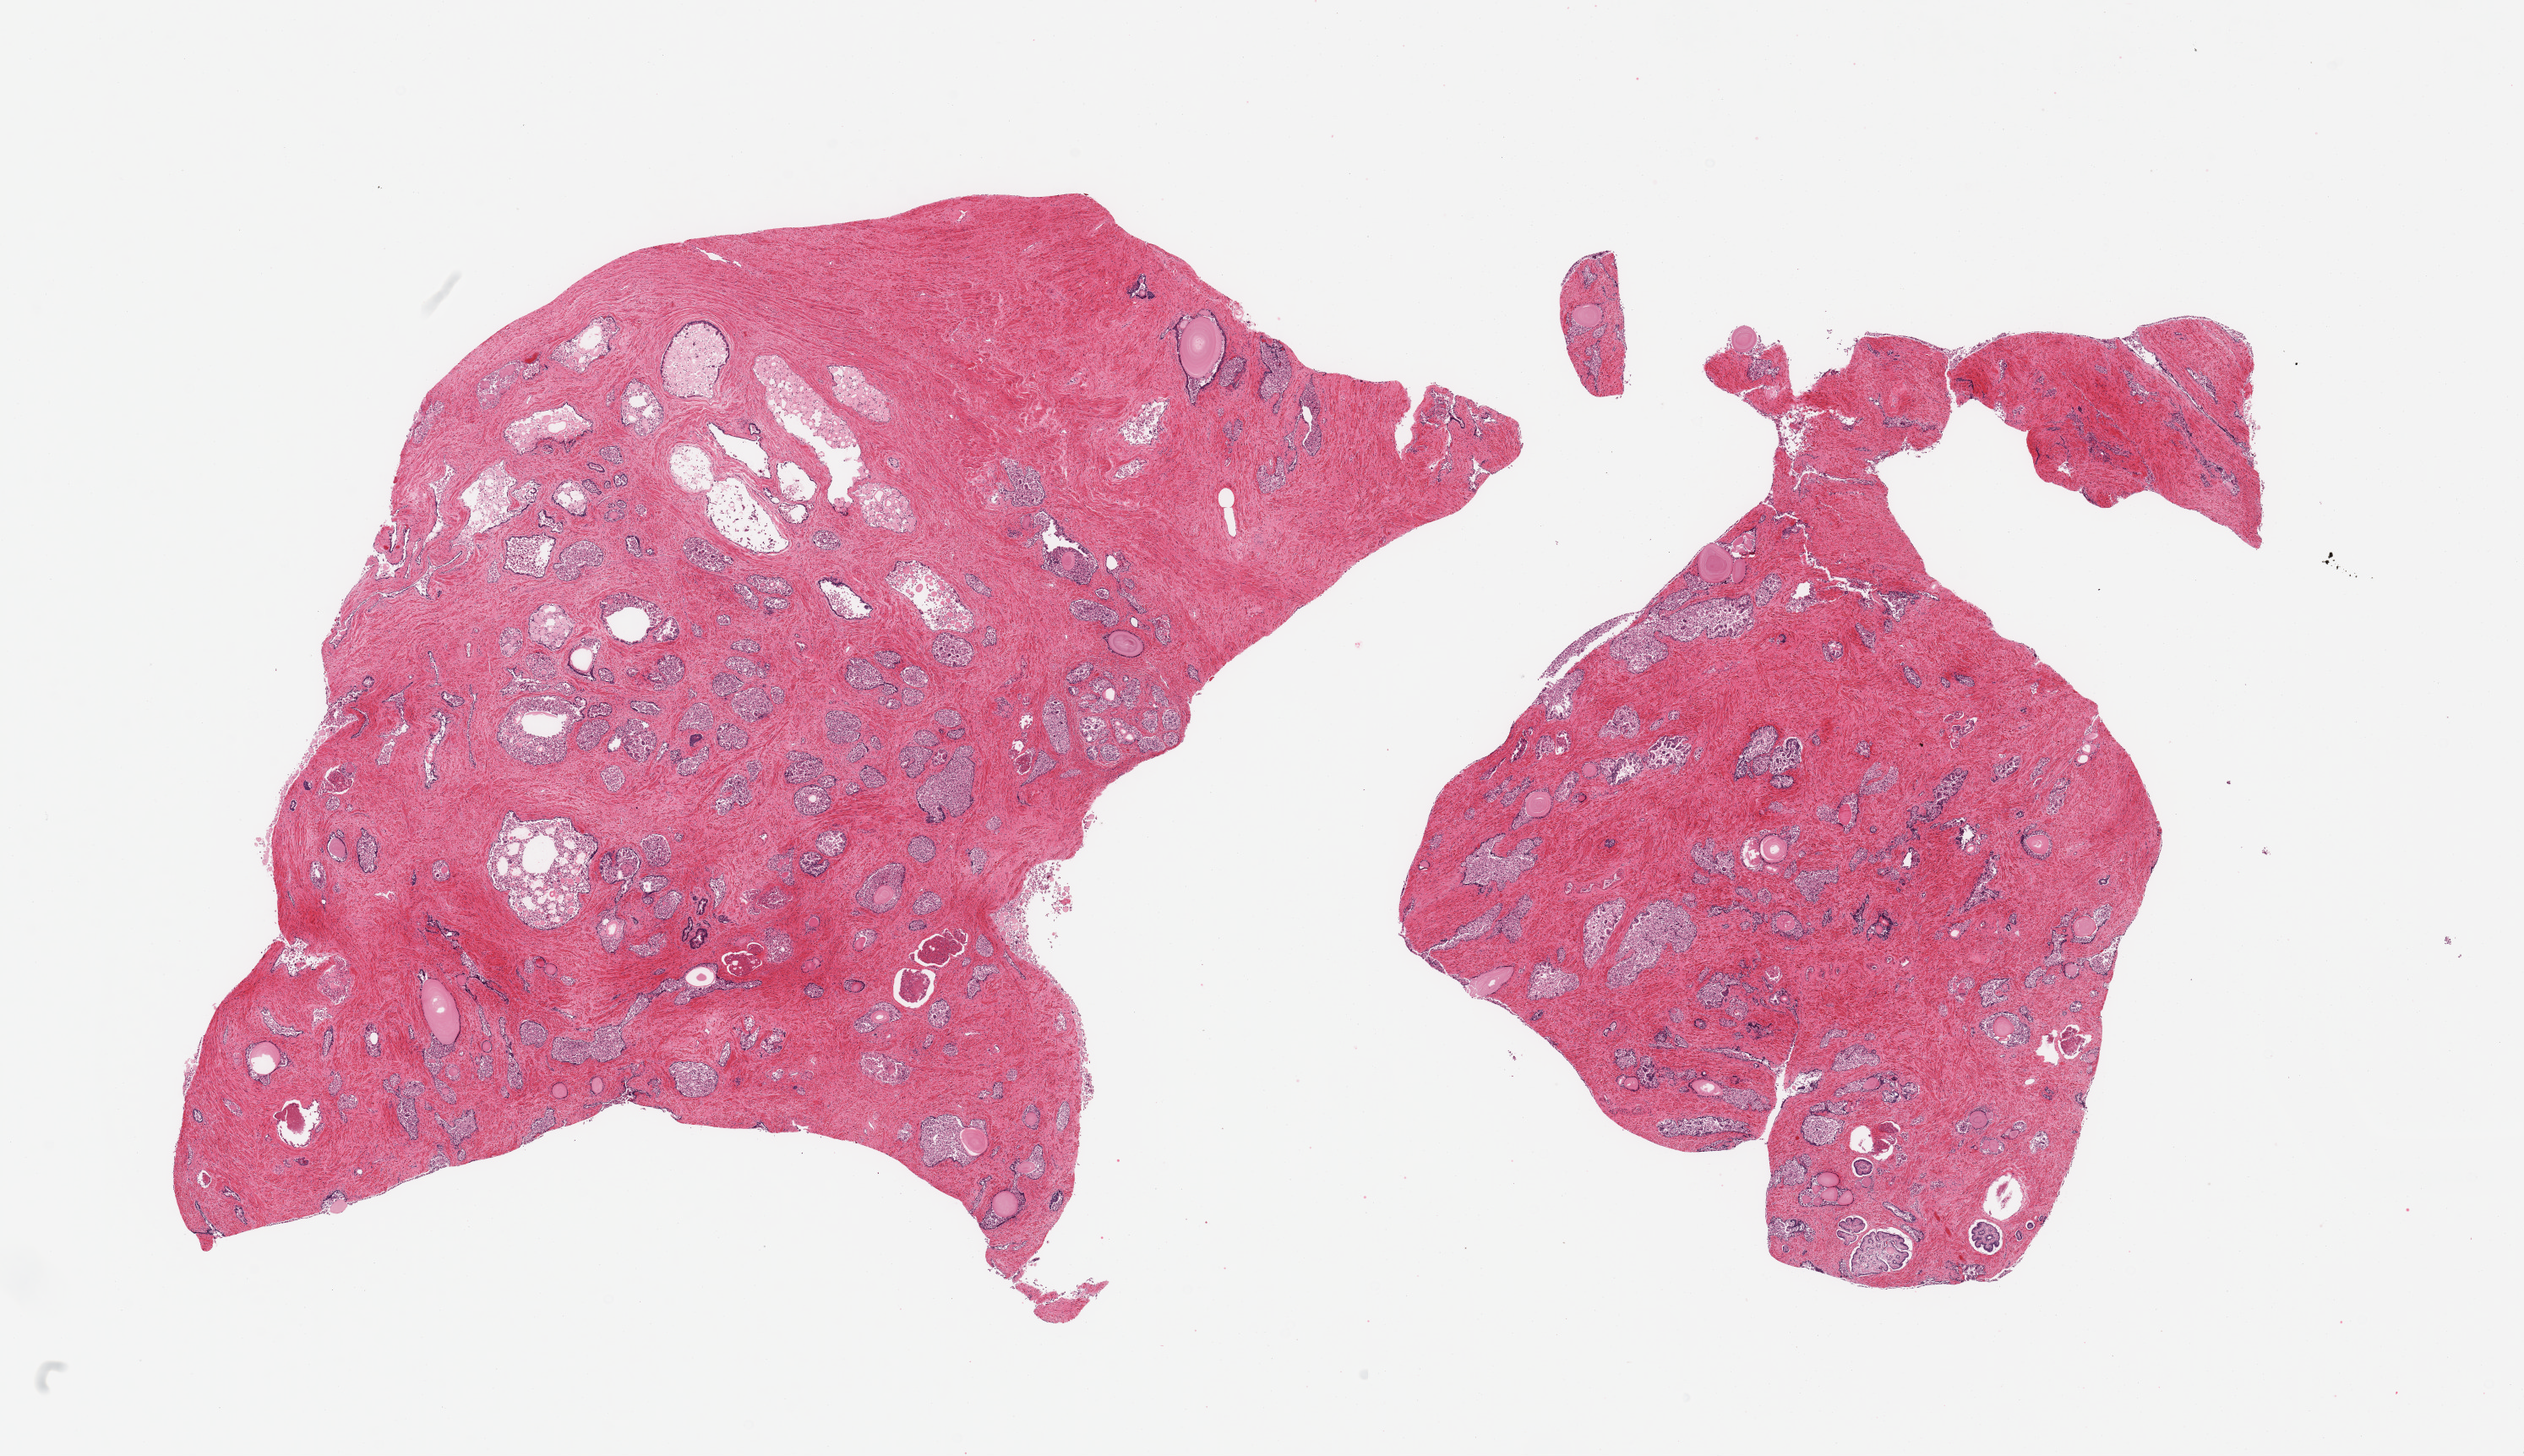
Haematoxylin and eosin whole-slide image, shown as a low-resolution overview of the whole scanned area (about 23.6 x 13.6 mm, slide scanned at 20x); PAXgene-fixed, paraffin-embedded tissue; sampled site (target tissue): prostate; tissue donor sample. Donor: male.
• reviewer comment on this tissue sample: 2 pieces; fibromuscular stroma and glands with sloughed epithelium and corpora amylacea